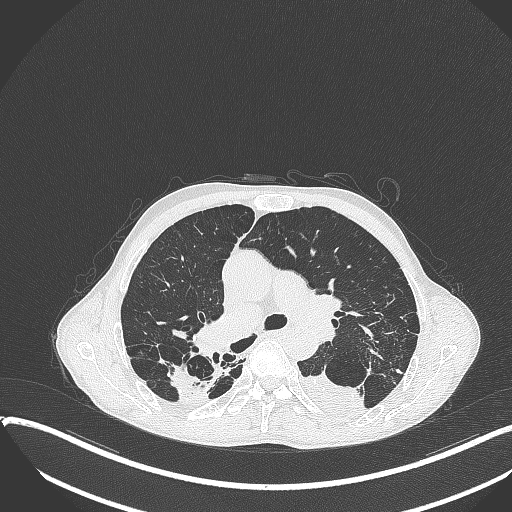
Chest CT, one axial slice. Slice 243 of 401 in the series (ordered by position). 120 kVp. Lung window (W 1500 / L -600 HU). 1 mm slice thickness. 512 × 512 image matrix, field of view 400 × 400 mm. Patient: male, 57 years. From the clinical record (not read from this slice): clinical TNM (as recorded): T4 N0 M0.
Structures marked on this image (bounding box drawn by a radiologist):
- lung tumour (recorded histology: squamous cell carcinoma): box from (x=303, y=366) to (x=370, y=419) px